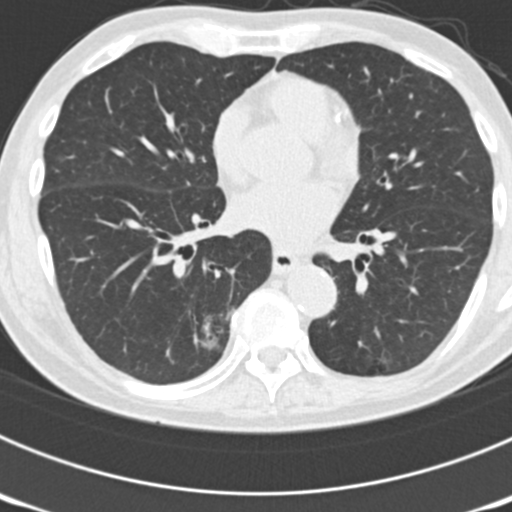
Axial slice from a low-dose chest CT screening exam. Third annual screen. Lung window (W 1500 / L -600 HU). Slice 89 of 177 in the series. Male, age 70 years at enrolment. Current smoker at enrolment.
- Lesion marked by an expert reader, bounding box [x1, y1, x2, y2] px = [150, 299, 239, 384].
- The screening reader recorded 3 non-calcified nodules or masses ≥4 mm on this exam (right upper lobe, left upper lobe, right lower lobe); which of them this box marks is not recorded.
- Official screen result: positive, other.
- Participant outcome: lung cancer diagnosed 14 days after this screen — bronchiolo-alveolar adenocarcinoma, NOS, right lower lobe, poorly differentiated (G3), stage IB (AJCC 6th edition), 30 mm at pathology.